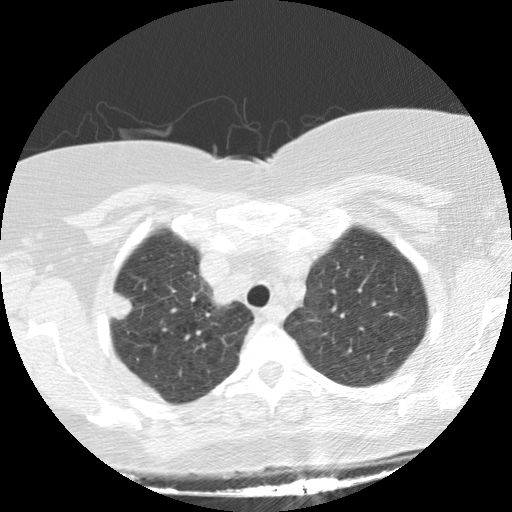
Low-dose screening chest CT, one axial slice. Slice 113 of 136 in the series (ordered by position). Reconstruction kernel STANDARD. 120 kVp. Lung window (W 1500 / L -600 HU). 512 × 512 image matrix, field of view 330 × 330 mm.
Outlined on this slice (expert manual segmentation):
- lesion 1 (tumor, upper lobe of right lung): bounding box <111,292,133,320> (left, top, right, bottom; pixels)